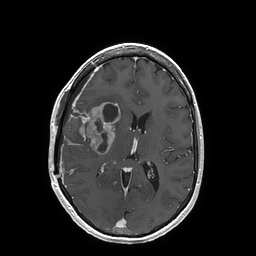
Brain MRI from a brain-tumour surgery series, one axial slice; slice 78 of 202 in the series (ordered by position); T1-weighted post-contrast; 1 mm slice thickness; 256 × 256 image matrix, field of view 250 × 250 mm. Case-level facts recorded for this patient, not image findings: histopathology: Glioblastoma; WHO grade: 4; IDH mutation: no.
Outlined on this slice (expert manual segmentation):
- tumour: bounding box [x1, y1, x2, y2] px = [69, 102, 121, 155]